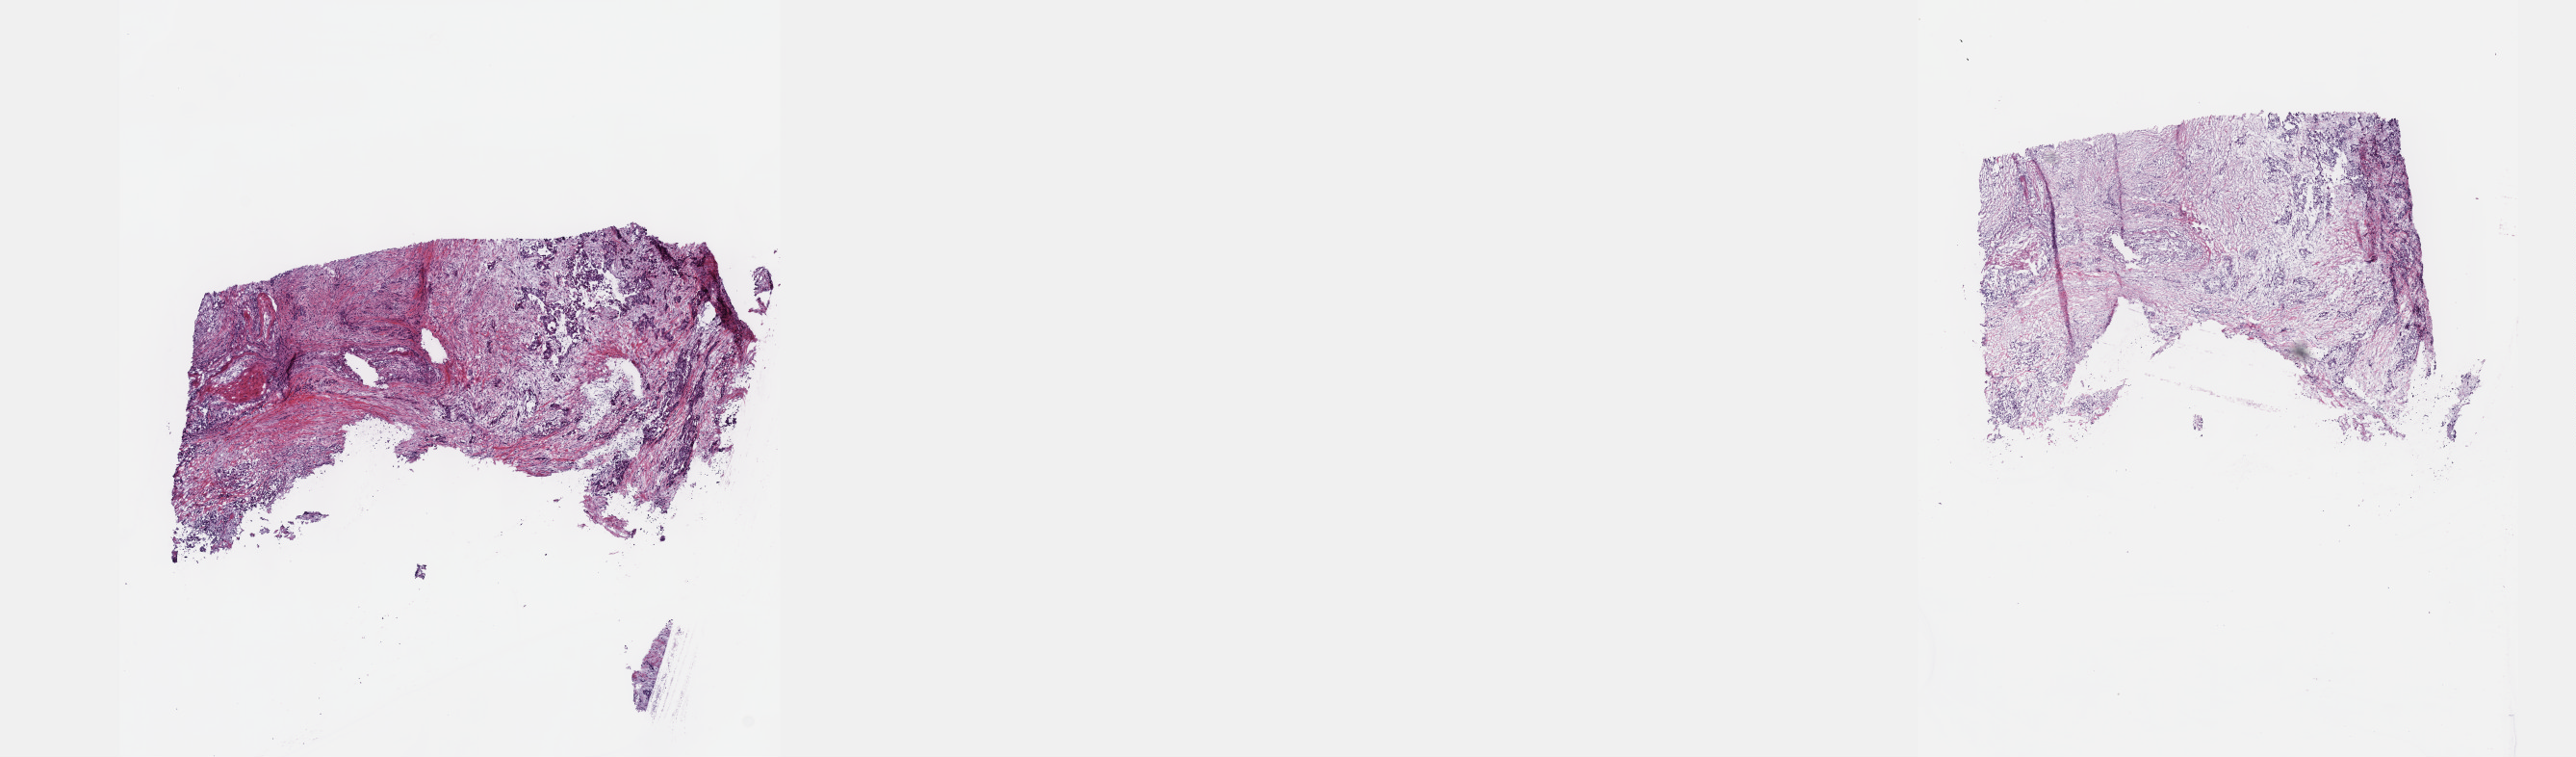
Digitized H&E-stained tissue section (whole slide) — a low-resolution overview of the entire scanned area, about 21.6 x 6.4 mm (slide scanned at 40x), frozen section from the top of the tissue portion, sample: primary tumour, pancreas. Male, age 75 years at initial diagnosis. Histologic grade: G2 (moderately differentiated). Pathologist review of this section (percent, as recorded): tumour cells 60%, tumour nuclei 60%, normal cells 0%, stromal cells 40%, necrosis 0%. Inflammatory infiltration, as recorded: lymphocyte infiltration 70%, monocyte infiltration 10%, neutrophil infiltration 10%.
Pathologic diagnosis: Infiltrating duct carcinoma, NOS (body of pancreas). AJCC pathologic stage: IIA (7th edition). TNM: T3 N0 M0.